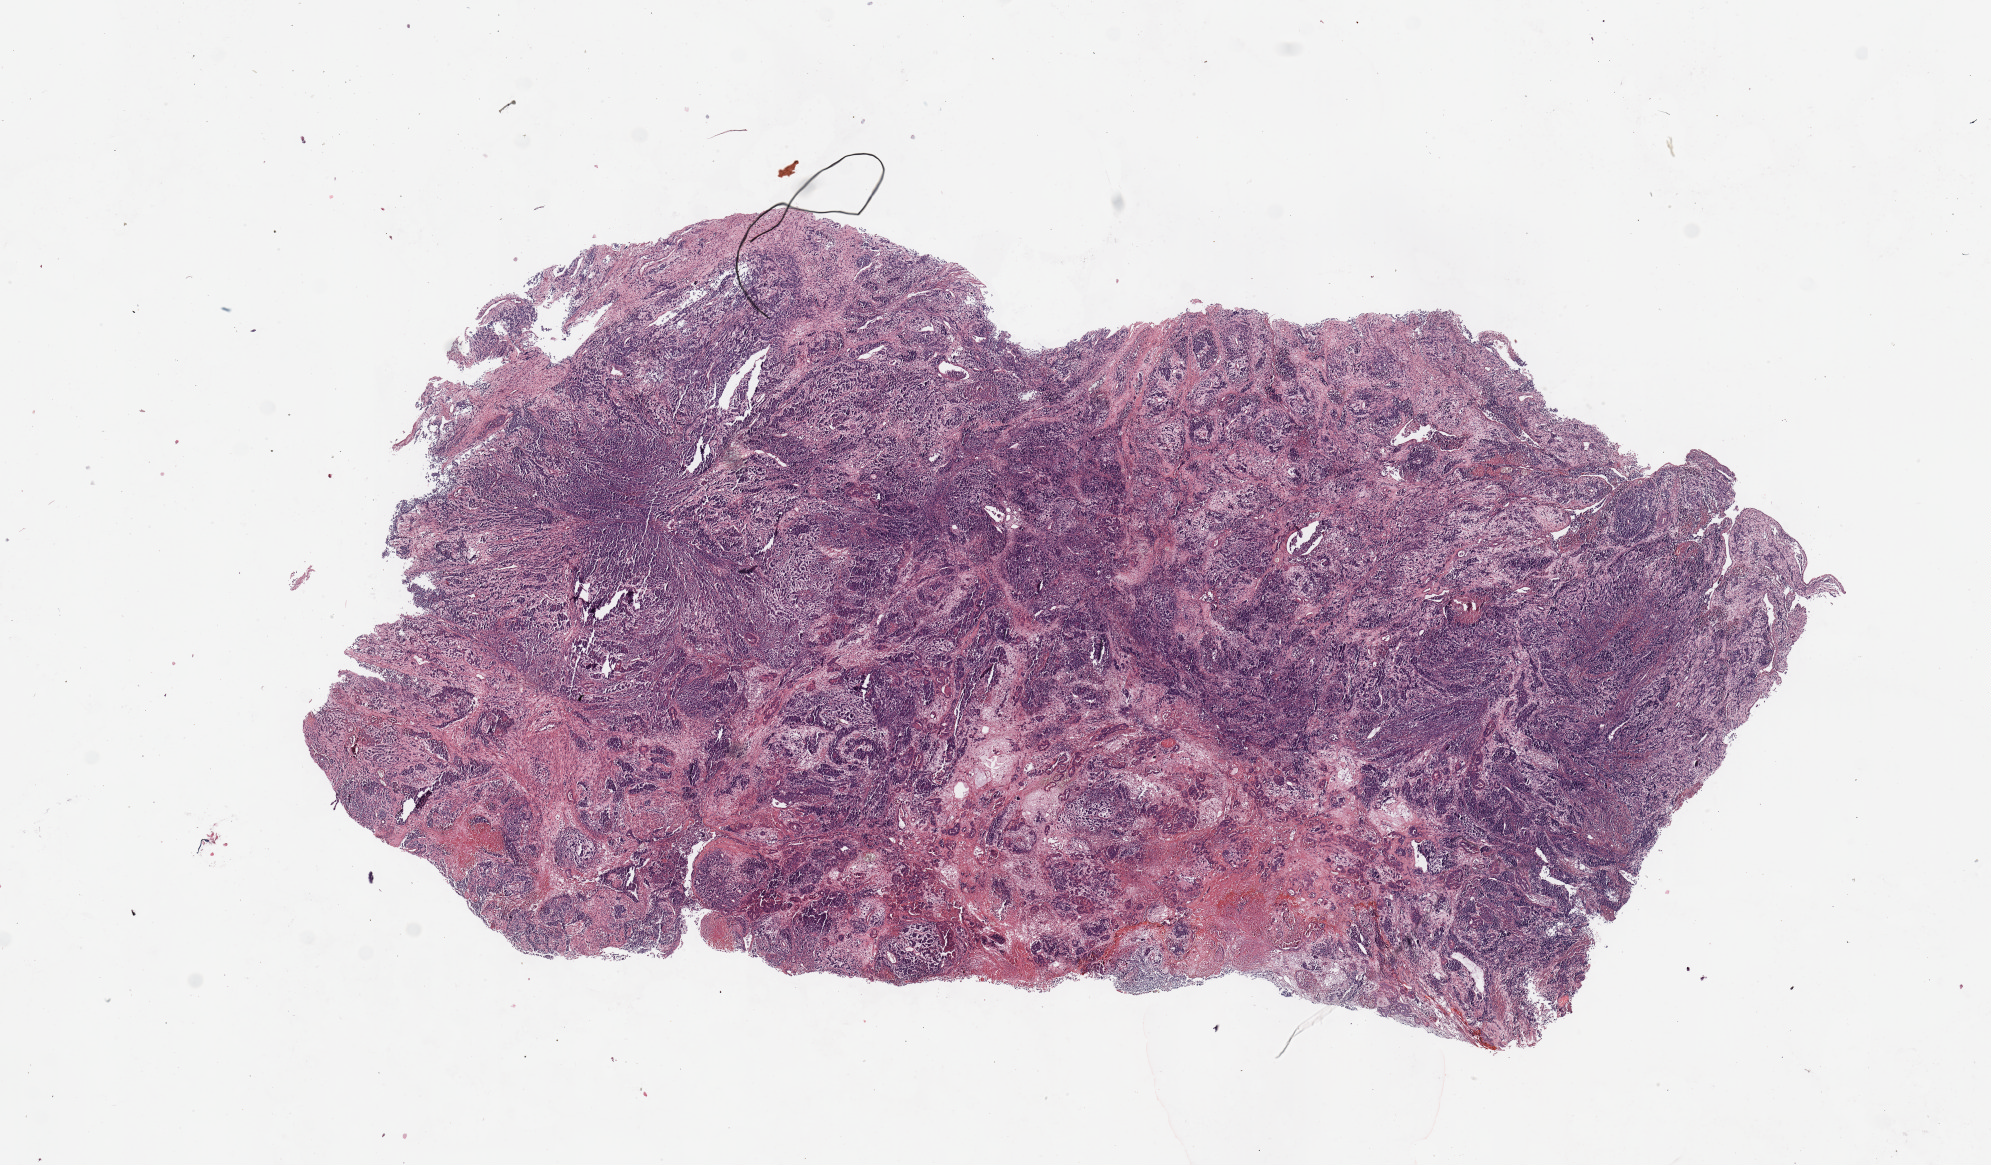
Whole-slide histology image, H&E-stained, shown as a low-resolution overview of the whole scanned area (about 15.8 x 9.2 mm), tumour tissue sample, sampled site: uterus. Patient: female, age 68 years. Histologic grade: G3 (poorly differentiated). Slide review estimates, as recorded: tumour nuclei 80%, necrosis 10%.
• AJCC pathologic stage: I
• histologic diagnosis: Endometrioid adenocarcinoma, NOS